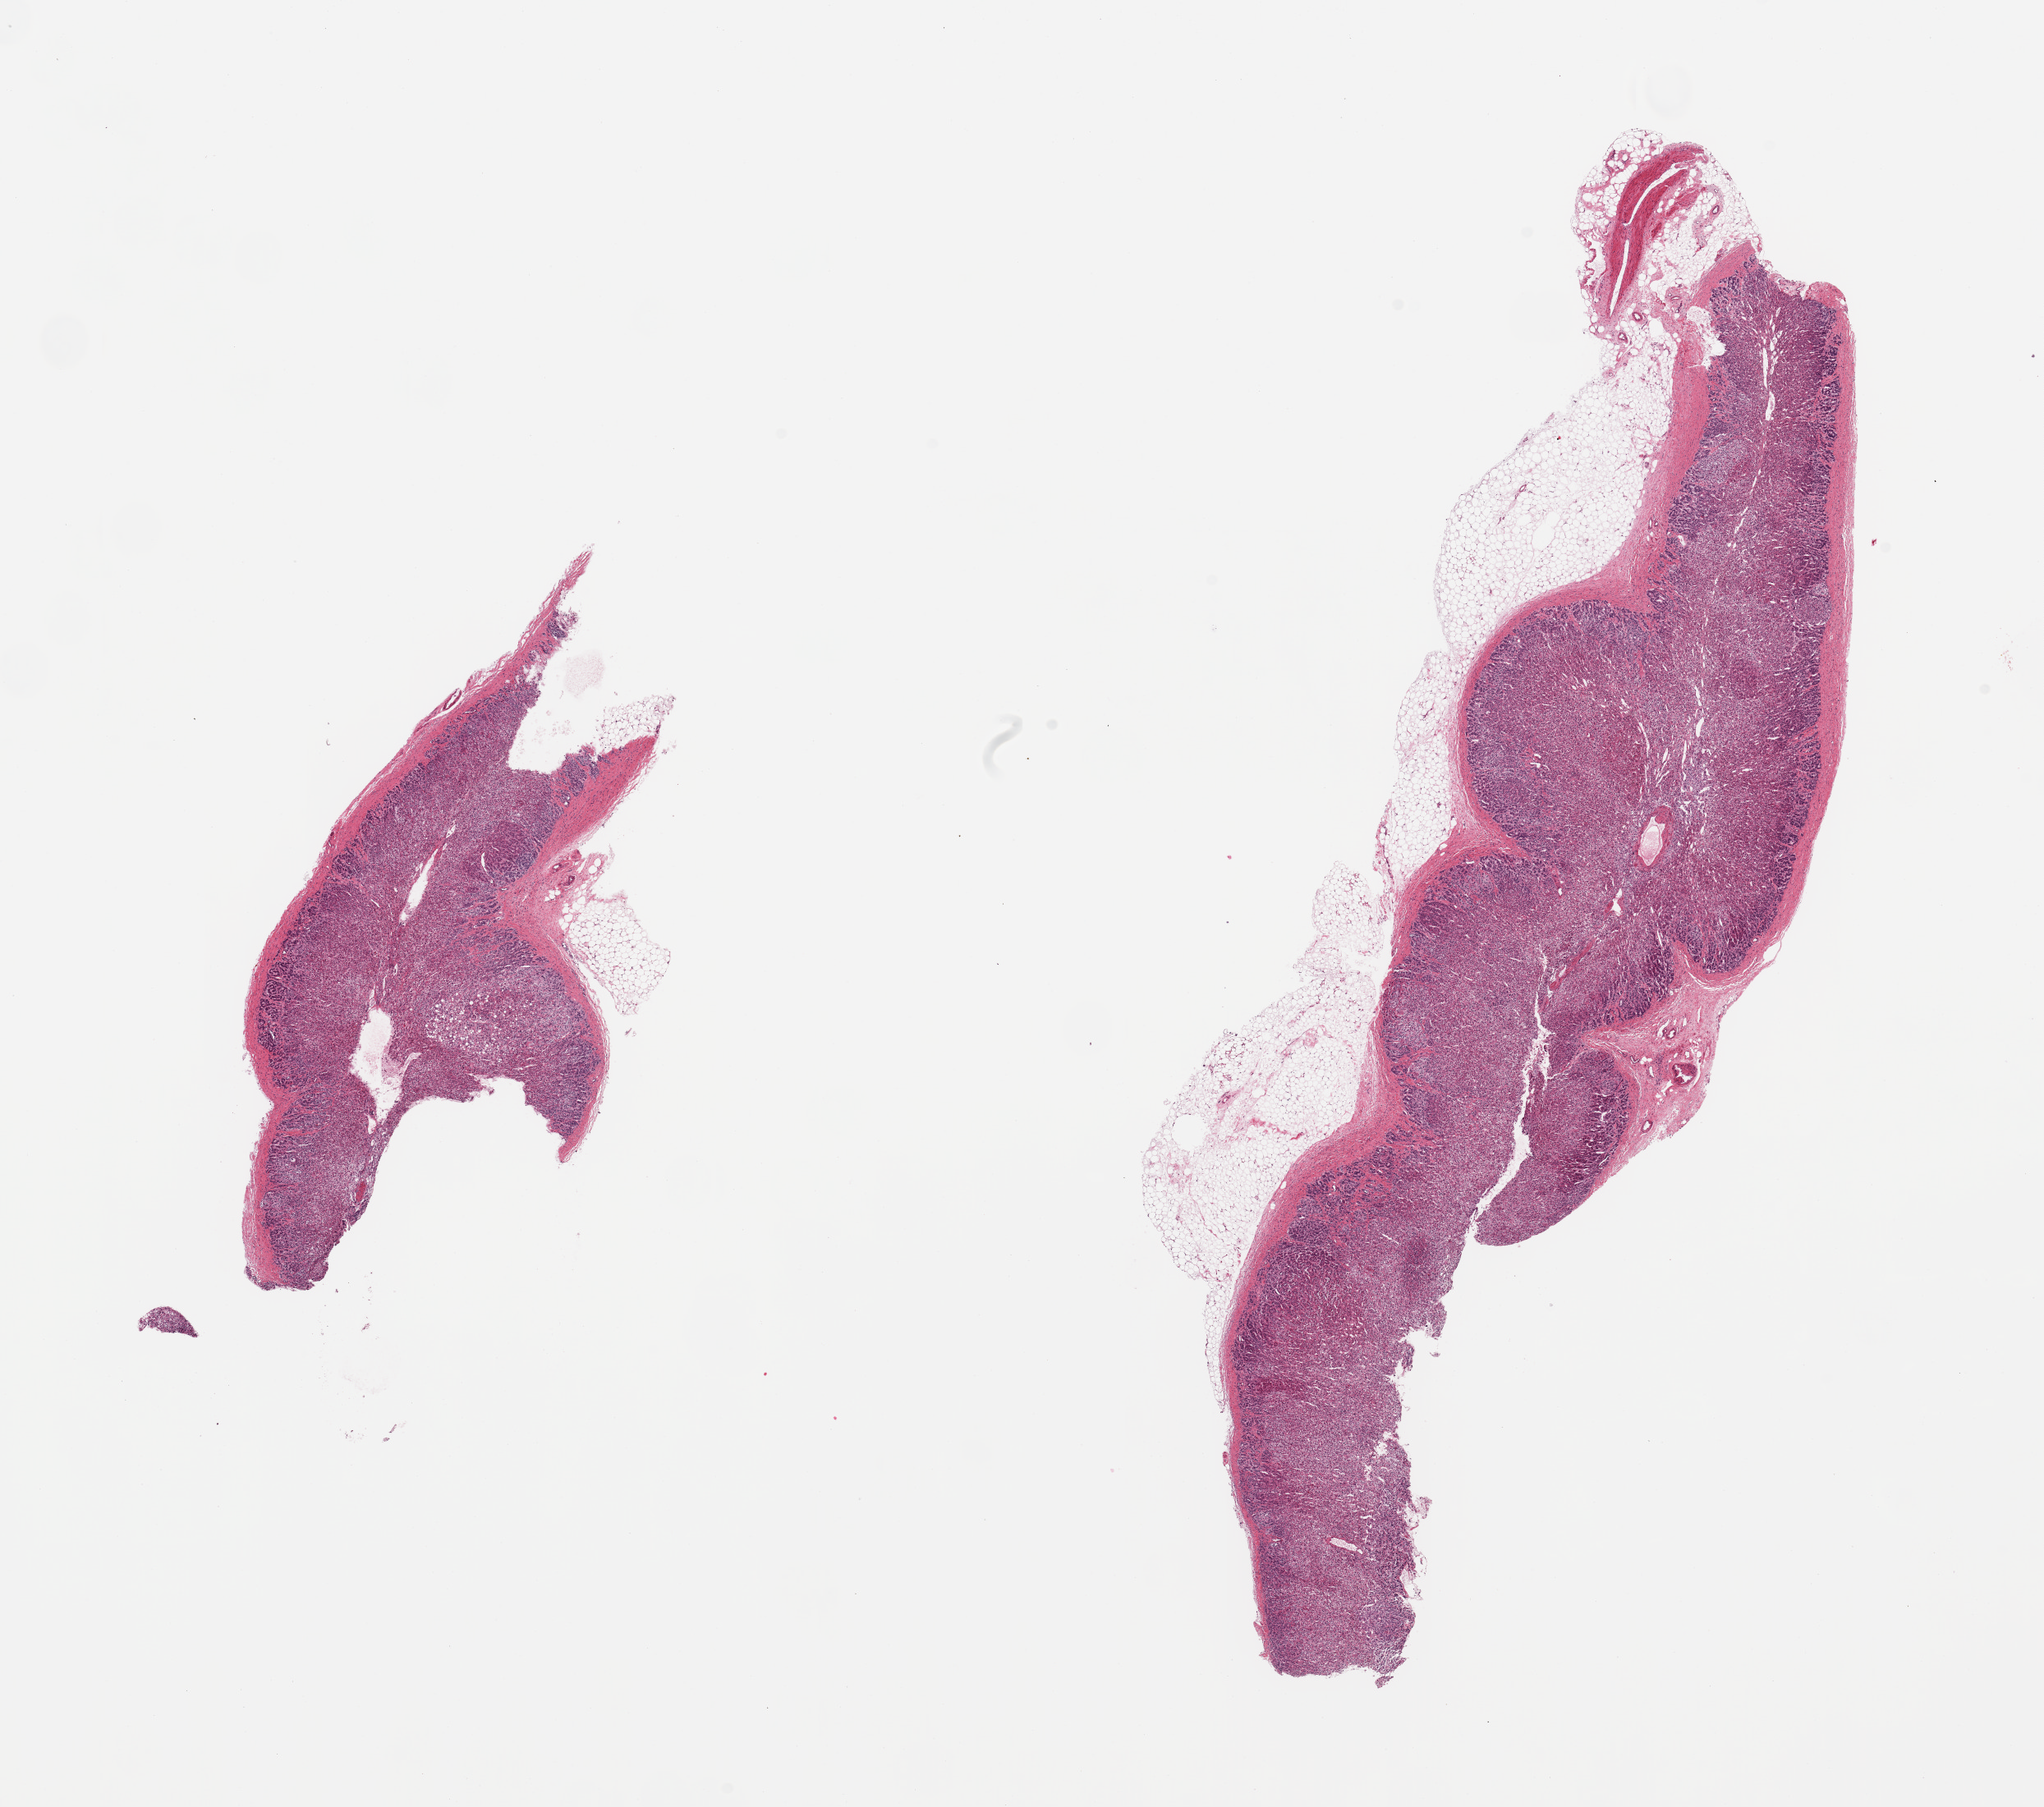
Haematoxylin and eosin whole-slide image, brightfield, whole scanned area (about 19.7 x 17.4 mm, from a 20x scan) shown as a low-resolution overview, PAXgene-fixed, paraffin-embedded tissue, target tissue: adrenal gland, tissue donor sample. Donor: female.
Review note (as recorded): 2 pieces; mostly cortex; 20% external fat.